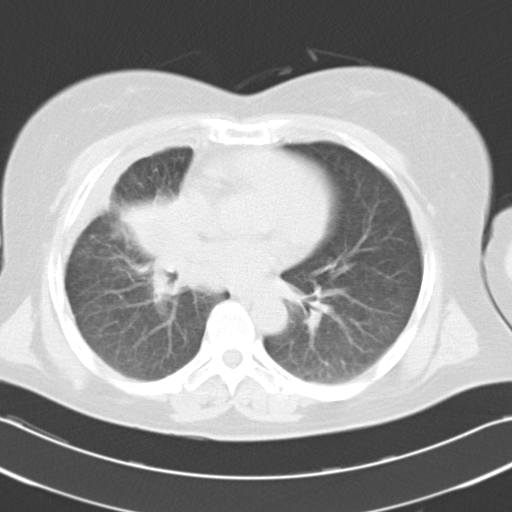
Chest CT, one axial slice. Position 8 of 19 along the scan axis. Reconstruction kernel B40f. 120 kVp. Lung window (W 1500 / L -600 HU). 10 mm slice thickness. 512 × 512 image matrix, field of view 346 × 346 mm. Patient: female, 52 years. From the clinical record (not read from this slice): clinical TNM (as recorded): T3 N1 M0.
Annotated regions visible in this slice (rectangle marked by the reading radiologist):
- lung tumour (recorded histology: squamous cell carcinoma): bounding box [x1, y1, x2, y2] px = [118, 186, 201, 307]